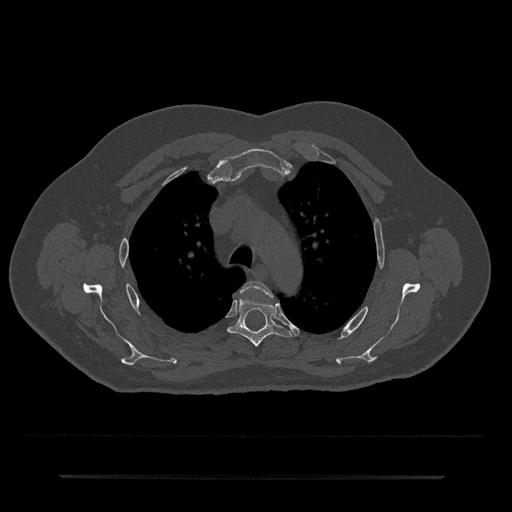
CT including the spine, one axial slice; slice 533 of 797 in the series (ordered by position); reconstruction kernel Br40s/3; bone window (W 1800 / L 400 HU); 512 × 512 image matrix, field of view 437 × 437 mm. Patient: male, 69 years. Case-level facts recorded for this patient, not image findings: primary cancer: prostate.
Outlined on this slice (semi-automatic segmentation, software-assisted and operator-edited):
- T3 vertebra: bounding box [x1, y1, x2, y2] px = [241, 281, 273, 297]
- T4 vertebra: [228, 299, 291, 347]